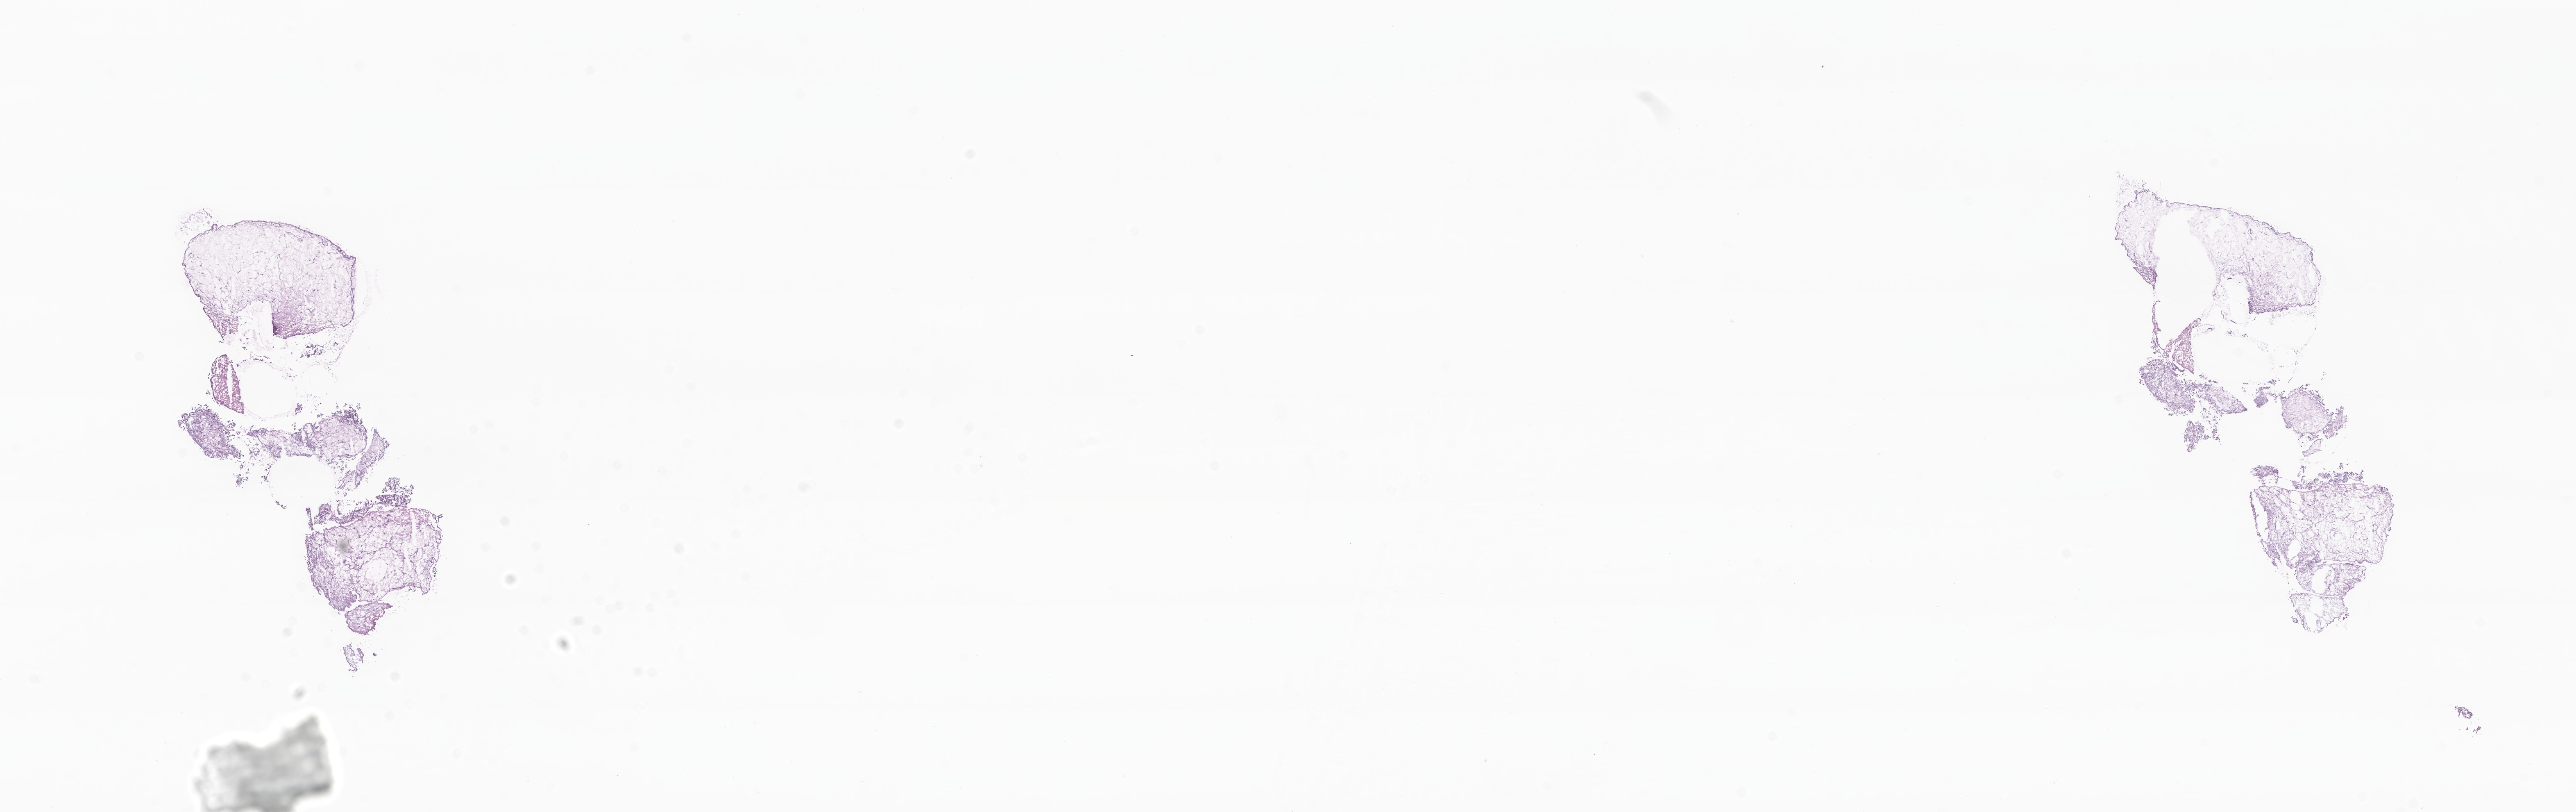
Whole-slide image, haematoxylin and eosin stain of tumor tissue from the cerebral ventricle, low-resolution overview of the scanned area, about 26.5 x 8.4 mm. Cryosection (OCT / tissue freezing medium). Patient male; age 131 days.
Diagnosis (ICD-O-3 morphology term): Choroid plexus papilloma, NOS.